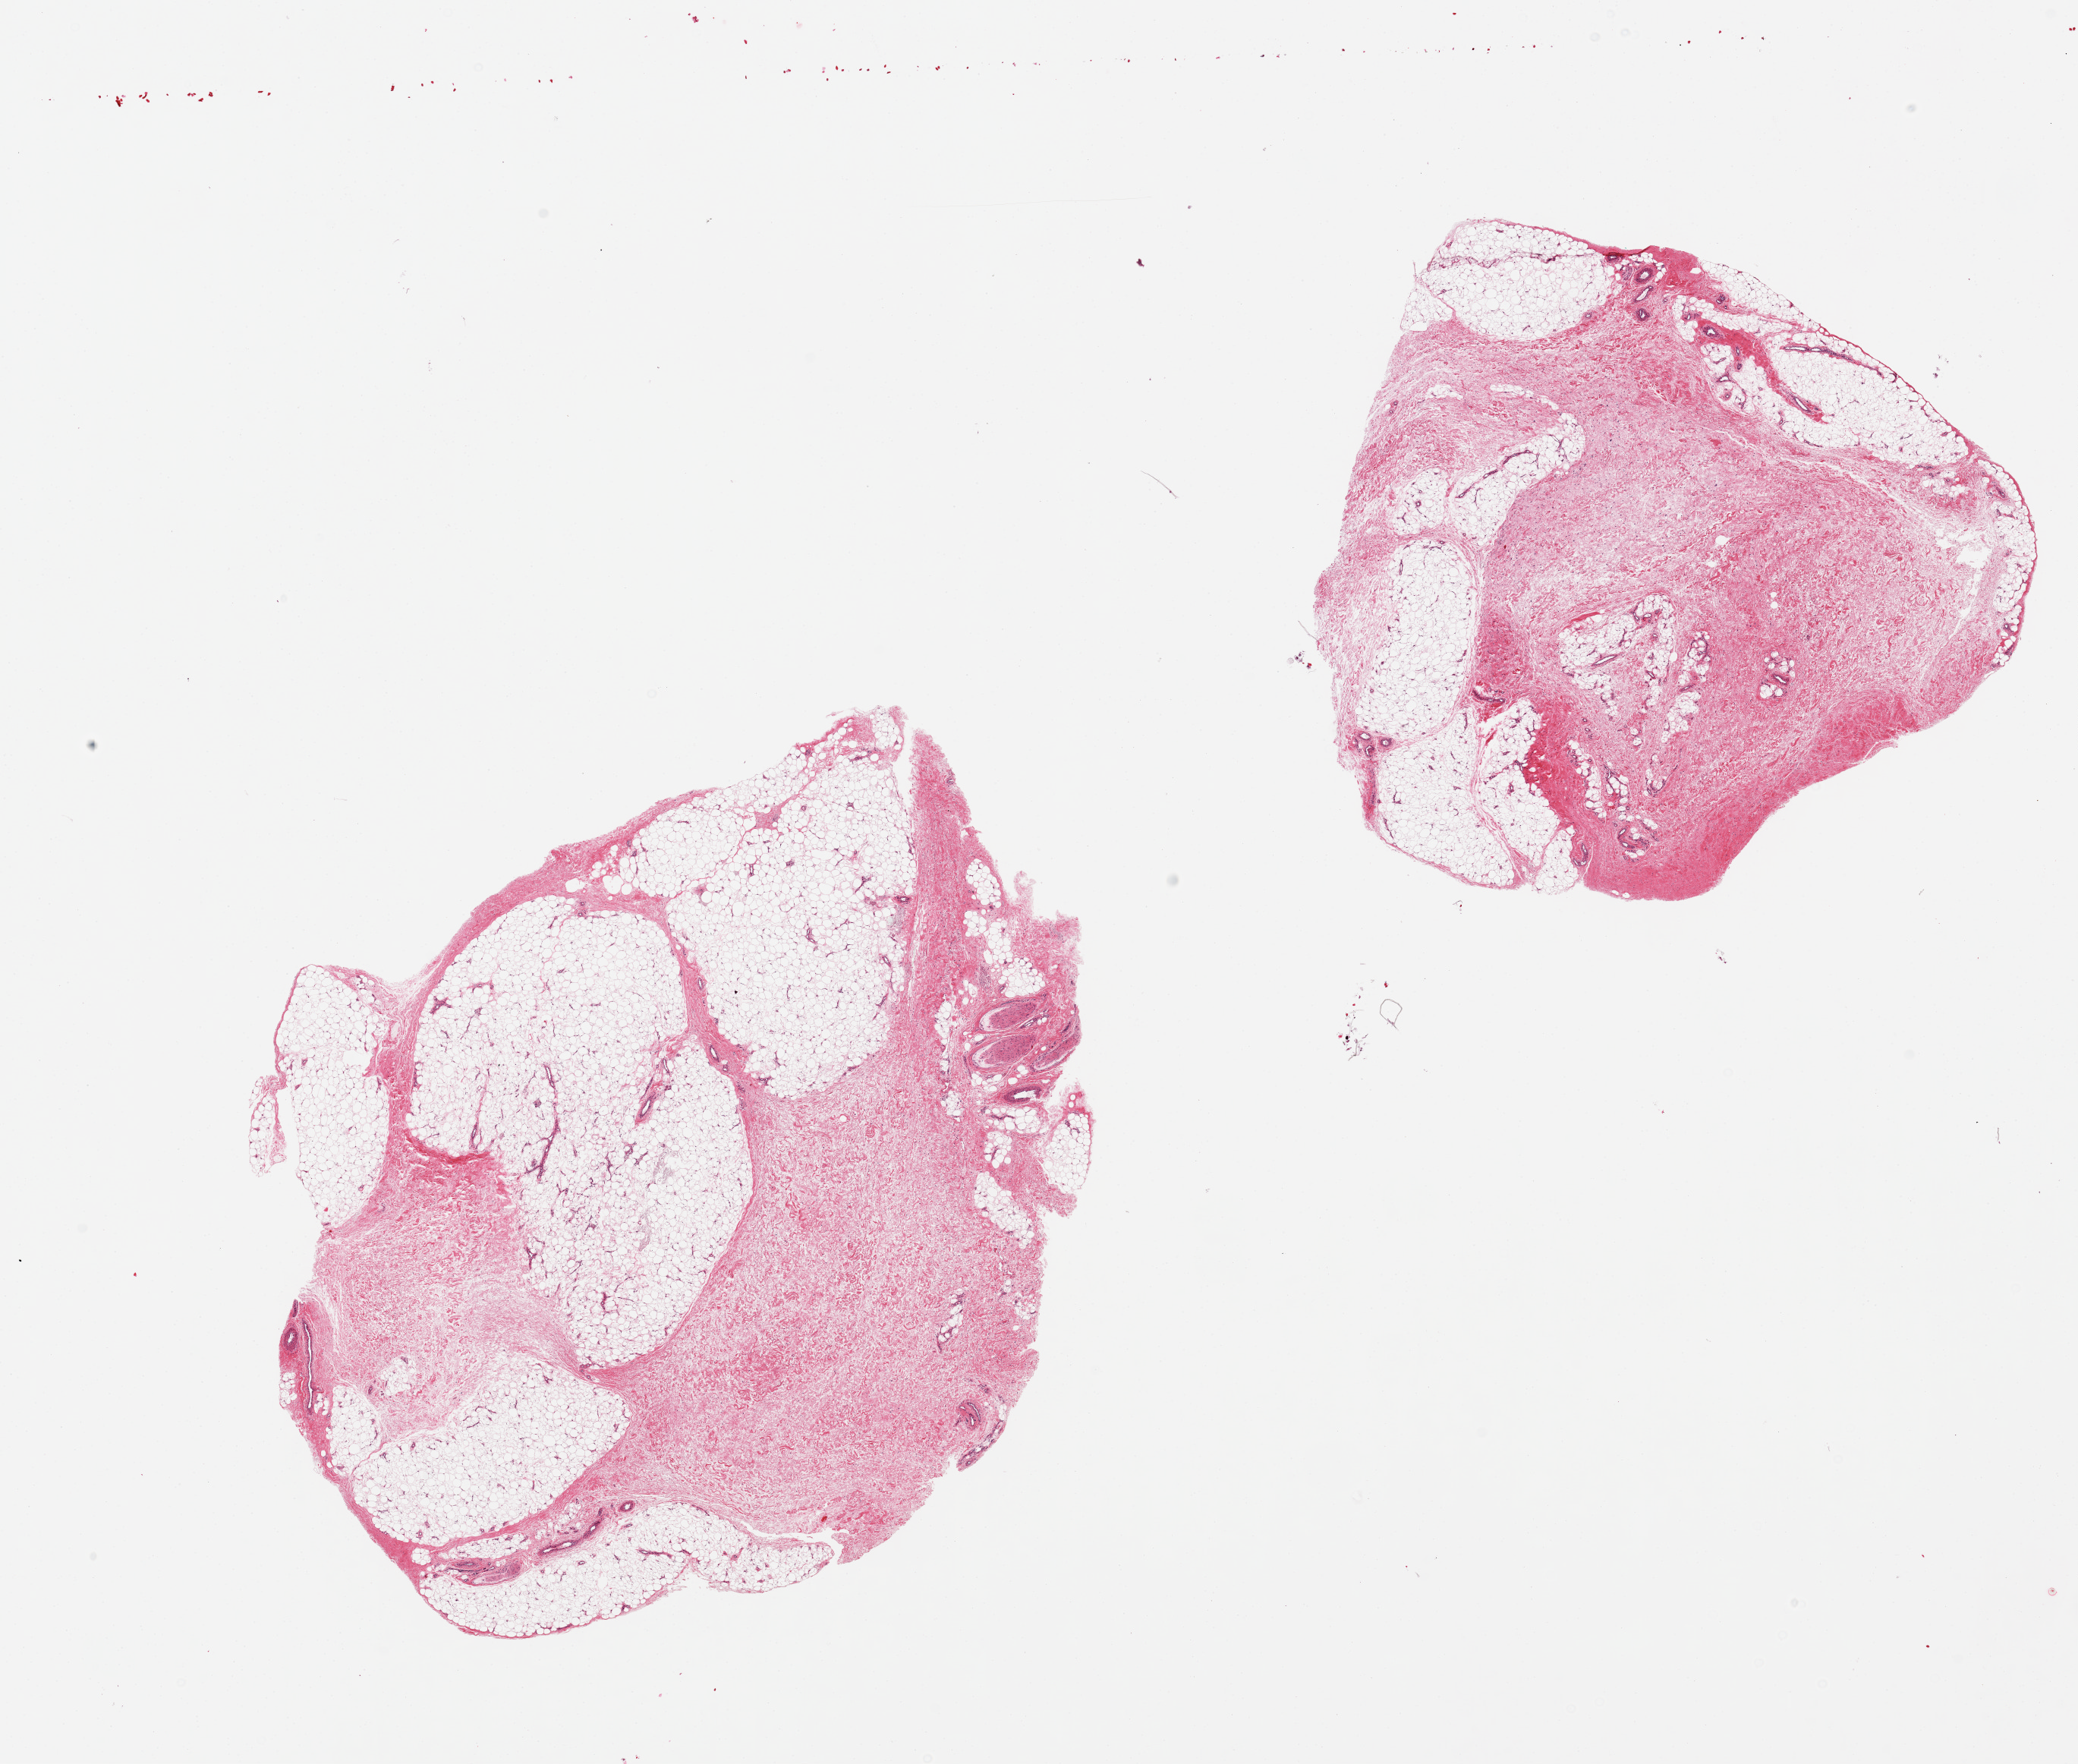
Whole-slide image, H&E stain, shown as a low-resolution overview of the whole scanned area (about 21.7 x 18.4 mm, slide scanned at 20x), PAXgene-fixed, paraffin-embedded tissue, target tissue: adipose tissue, donor tissue sample. Donor sex: male.
Review note (as recorded): 2 pieces, both ~60% contaminating fibroconnective tissue/fascia.